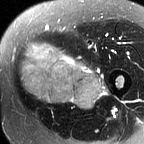
MRI of an extremity soft-tissue mass, one axial slice; position 24 of 60 along the scan axis; T2-weighted fat-saturated; MR volume resampled by the dataset authors to the PET/CT grid (not the native acquisition matrix); 3.27 mm slice thickness; 144 × 144 image matrix, field of view 141 × 141 mm. Female patient. Case-level facts recorded for this patient, not image findings: histological type: pleiomorphic leiomyosarcoma; grade: intermediate; site of the primary tumour: left thigh.
Annotated regions visible in this slice (expert contour drawn on MRI and transferred to this co-registered scan by the dataset authors):
- gross tumour volume including surrounding oedema: bounding box <18,42,108,109> (left, top, right, bottom; pixels)
- gross tumour volume (mass): <20,44,101,109>